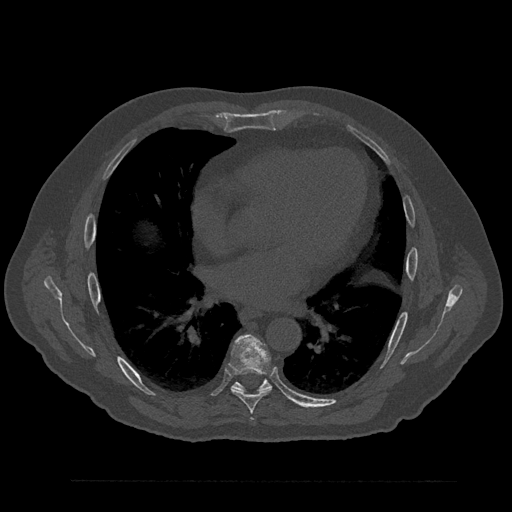
CT including the spine, one axial slice. Position 488 of 797 along the scan axis. 120 kVp. Bone window (W 1800 / L 400 HU). 512 × 512 image matrix. Patient: male, 61 years. Case-level facts recorded for this patient, not image findings: primary cancer: prostate.
Outlined on this slice (semi-automatic segmentation, software-assisted and operator-edited):
- T6 vertebra: bounding box <251,419,253,421> (left, top, right, bottom; pixels)
- T7 vertebra: <229,335,272,413>
- T8 vertebra: <232,378,272,392>